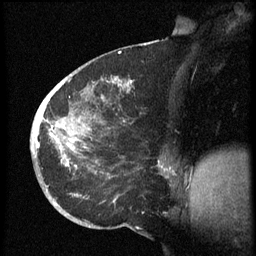
Breast MRI (dynamic contrast-enhanced), one sagittal slice; position 29 of 60 along the scan axis; dynamic contrast-enhanced series, image 2 of 3 at this slice position (ordered by acquisition); 1.5 T; TE 4.2 ms, TR 8.4 ms; 2.5 mm slice thickness; 256 × 256 image matrix, field of view 200 × 200 mm. Patient: female, 38 years. From the clinical record (not read from this slice): setting: breast cancer imaged before/during neoadjuvant chemotherapy; receptor status: HER2-positive.
Structures marked on this image (semi-automatic segmentation, software-assisted and operator-edited):
- analysis volume of interest (the breast-tissue region the enhancement analysis was run in; not a lesion): bounding box <31,74,173,202> (left, top, right, bottom; pixels)
- tumour enhancement mask (voxels above the 70 % enhancement threshold inside the analysis volume of interest): <34,77,172,172>